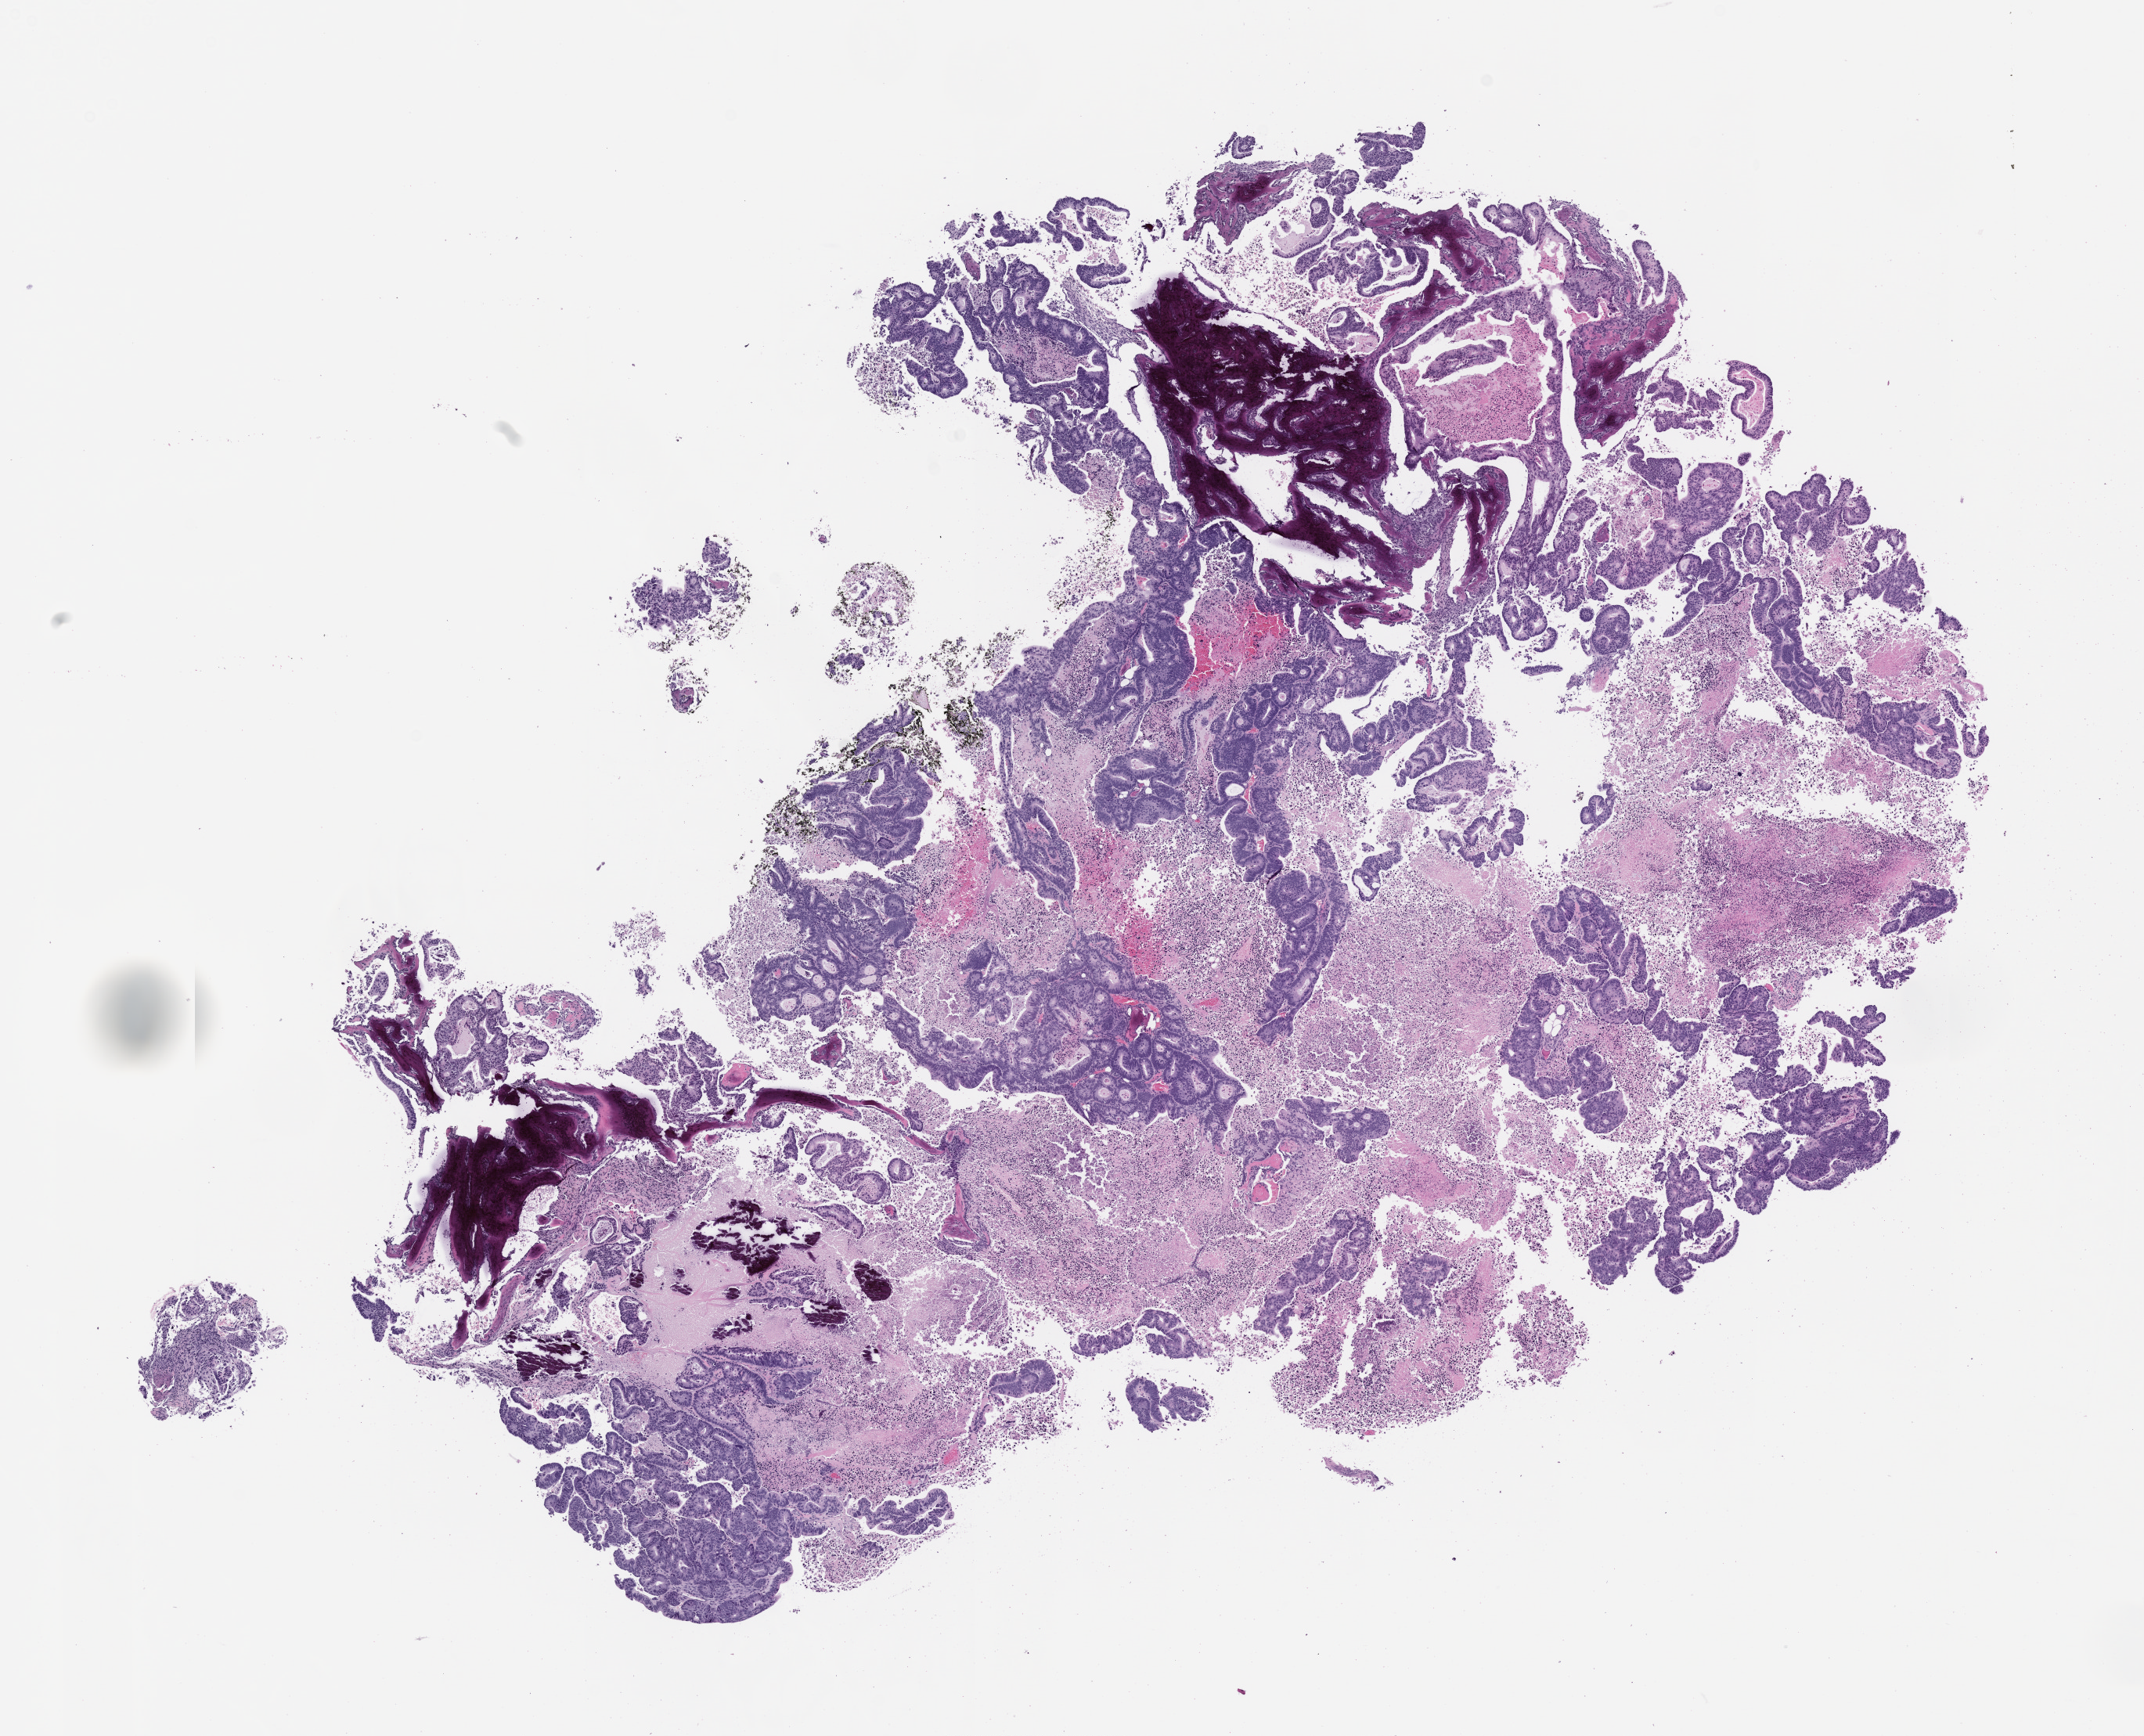
Haematoxylin and eosin whole-slide image of a patient-derived xenograft (PDX) tumor grown in a mouse, passage 0 — whole scanned area (about 11.0 x 8.9 mm) shown as a low-resolution overview, FFPE section, tumor site category: colon.
Originating patient diagnosis: Colon Adenocarcinoma.